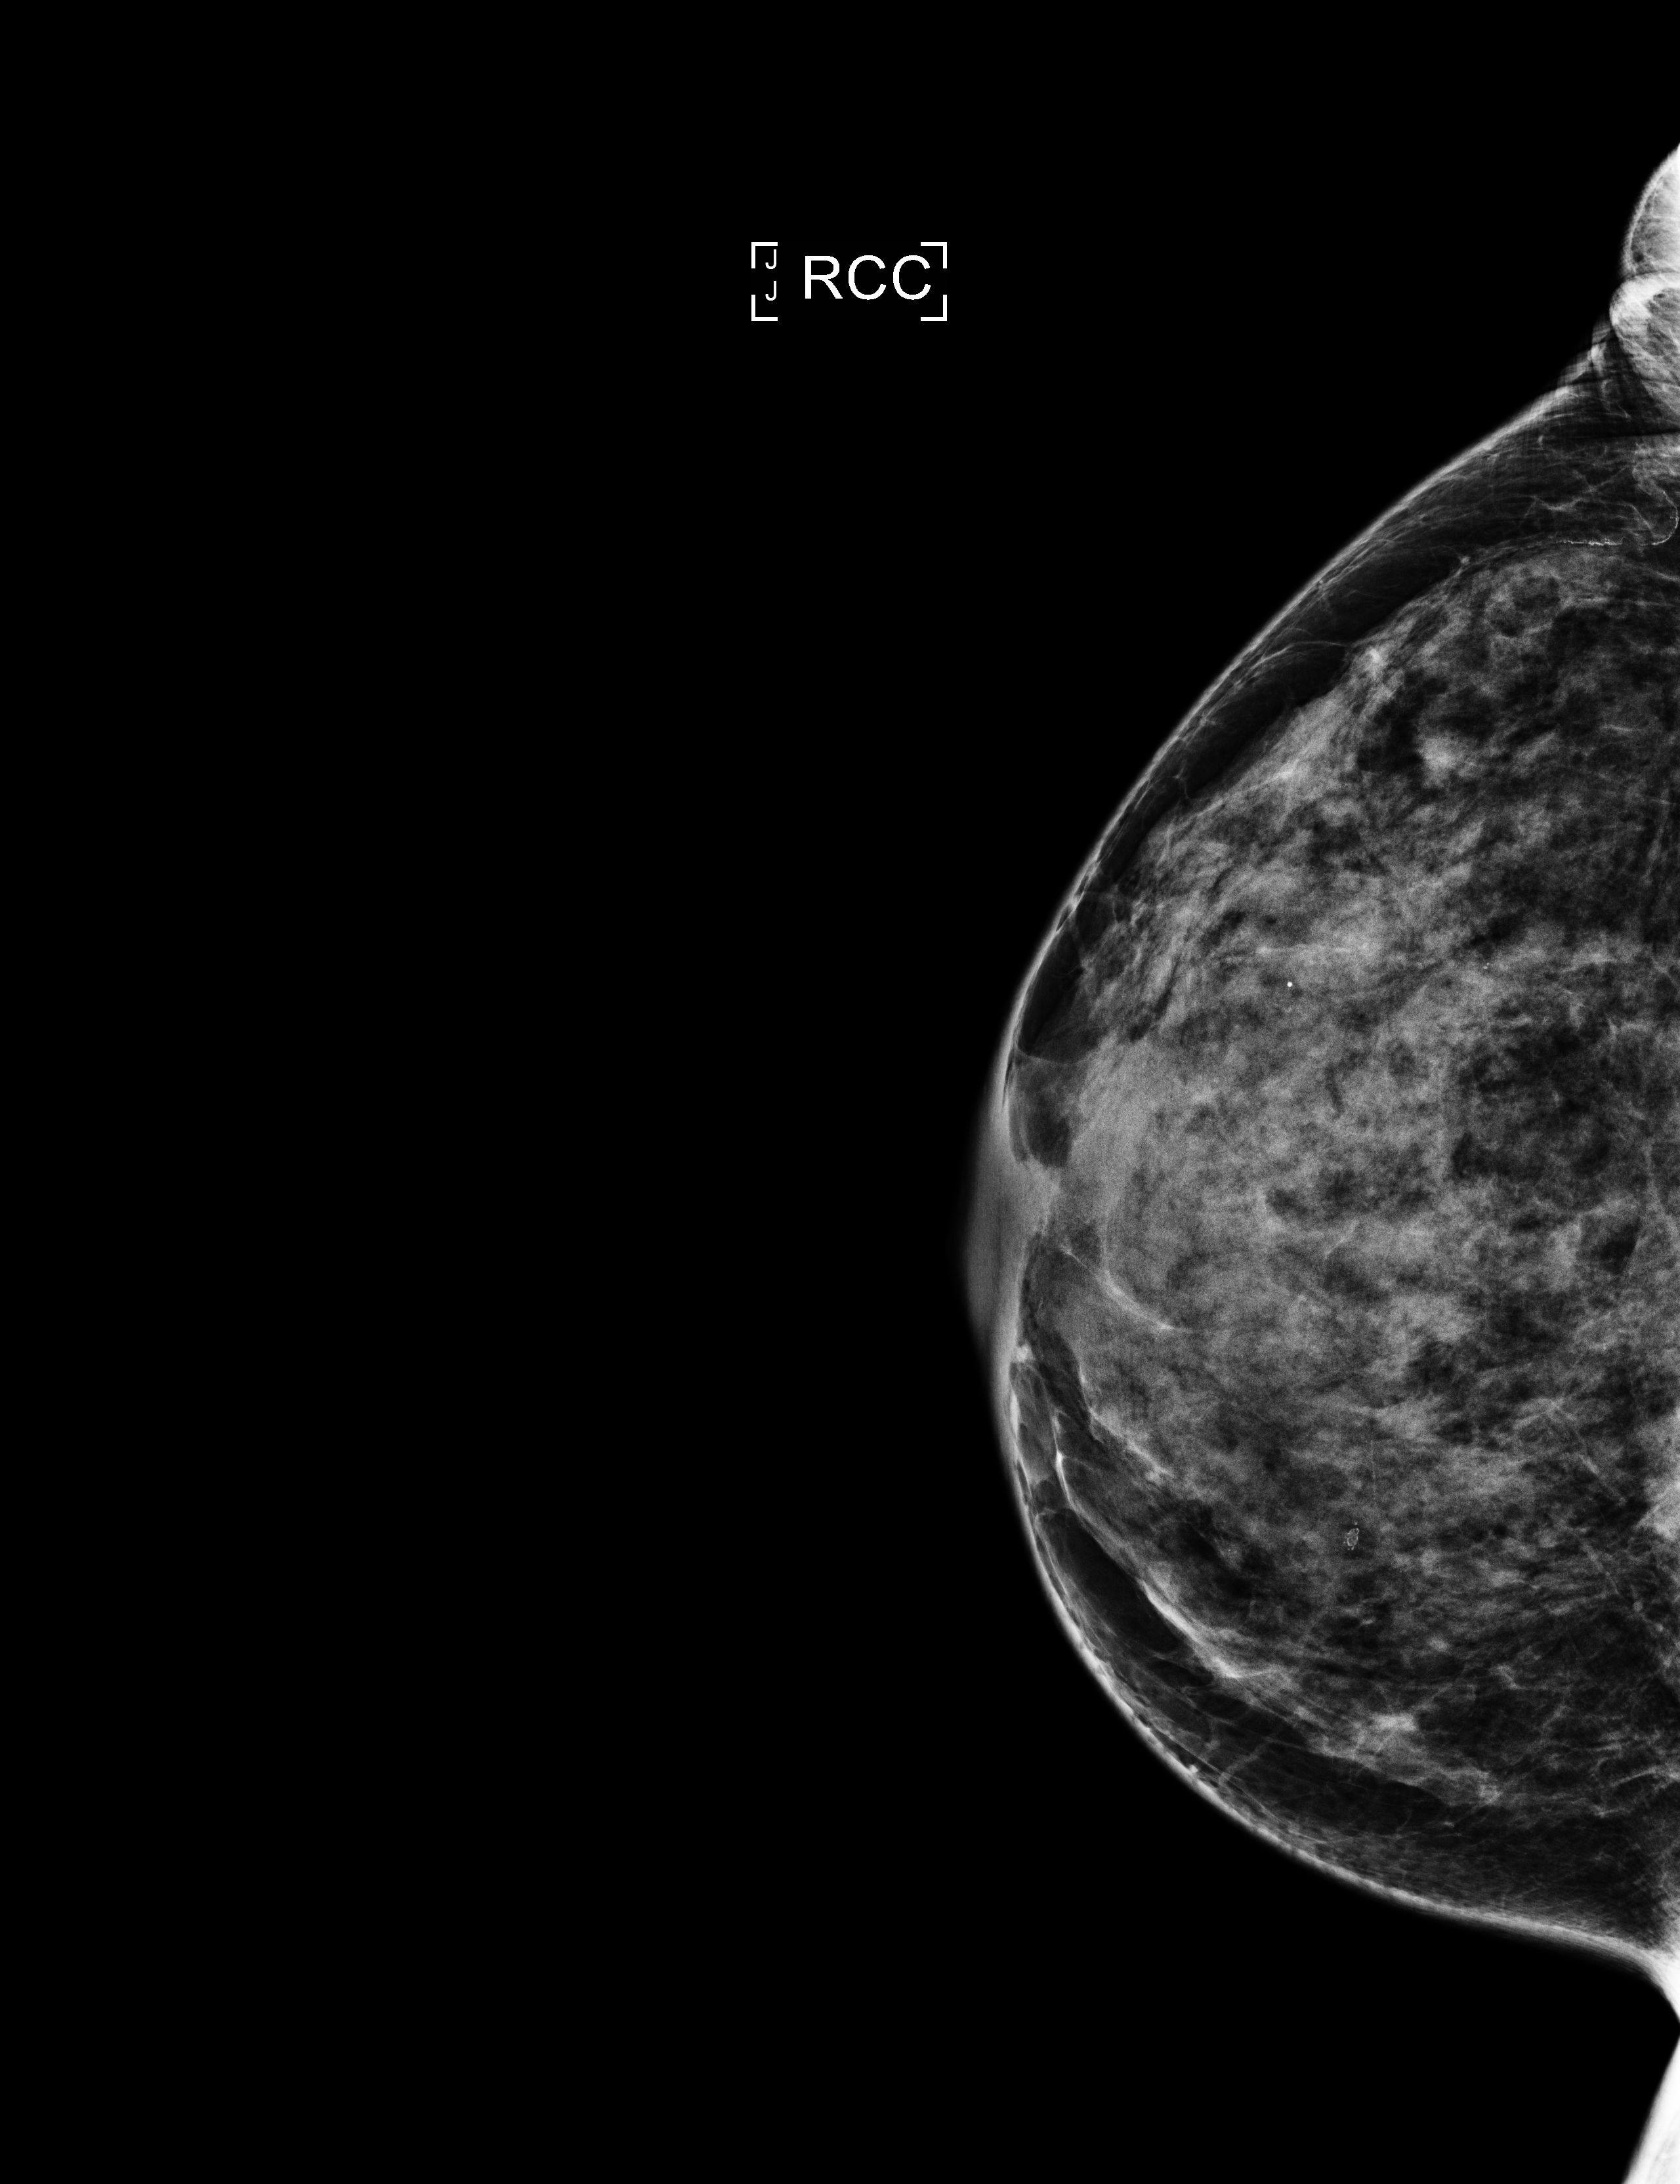
Digital mammogram (FFDM), right breast, craniocaudal (CC) view, annual screening mammography examination, compressed breast thickness 43 mm. Patient: female, 56 years.
BI-RADS breast density category at the screening exam (both breasts, scale 1–4): 1. Final BI-RADS assessment for this screening round (tomosynthesis exam, both breasts): category 1. Recall: no recall after this screen.